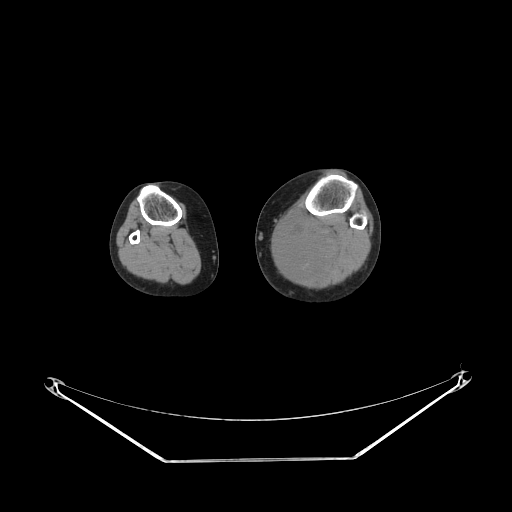
CT of an extremity soft-tissue mass (from a PET/CT study), one axial slice; slice 154 of 223 in the series (ordered by position); soft-tissue window (W 400 / L 40 HU); 512 × 512 image matrix. Female patient. Case-level facts recorded for this patient, not image findings: histological type: extraskeletal high grade osteogenic sarcoma; grade: high; site of the primary tumour: left calf.
Annotated regions visible in this slice (expert contour drawn on MRI and transferred to this co-registered scan by the dataset authors):
- gross tumour volume (mass): bounding box (x1, y1, x2, y2) in pixels: (274, 217, 339, 277)